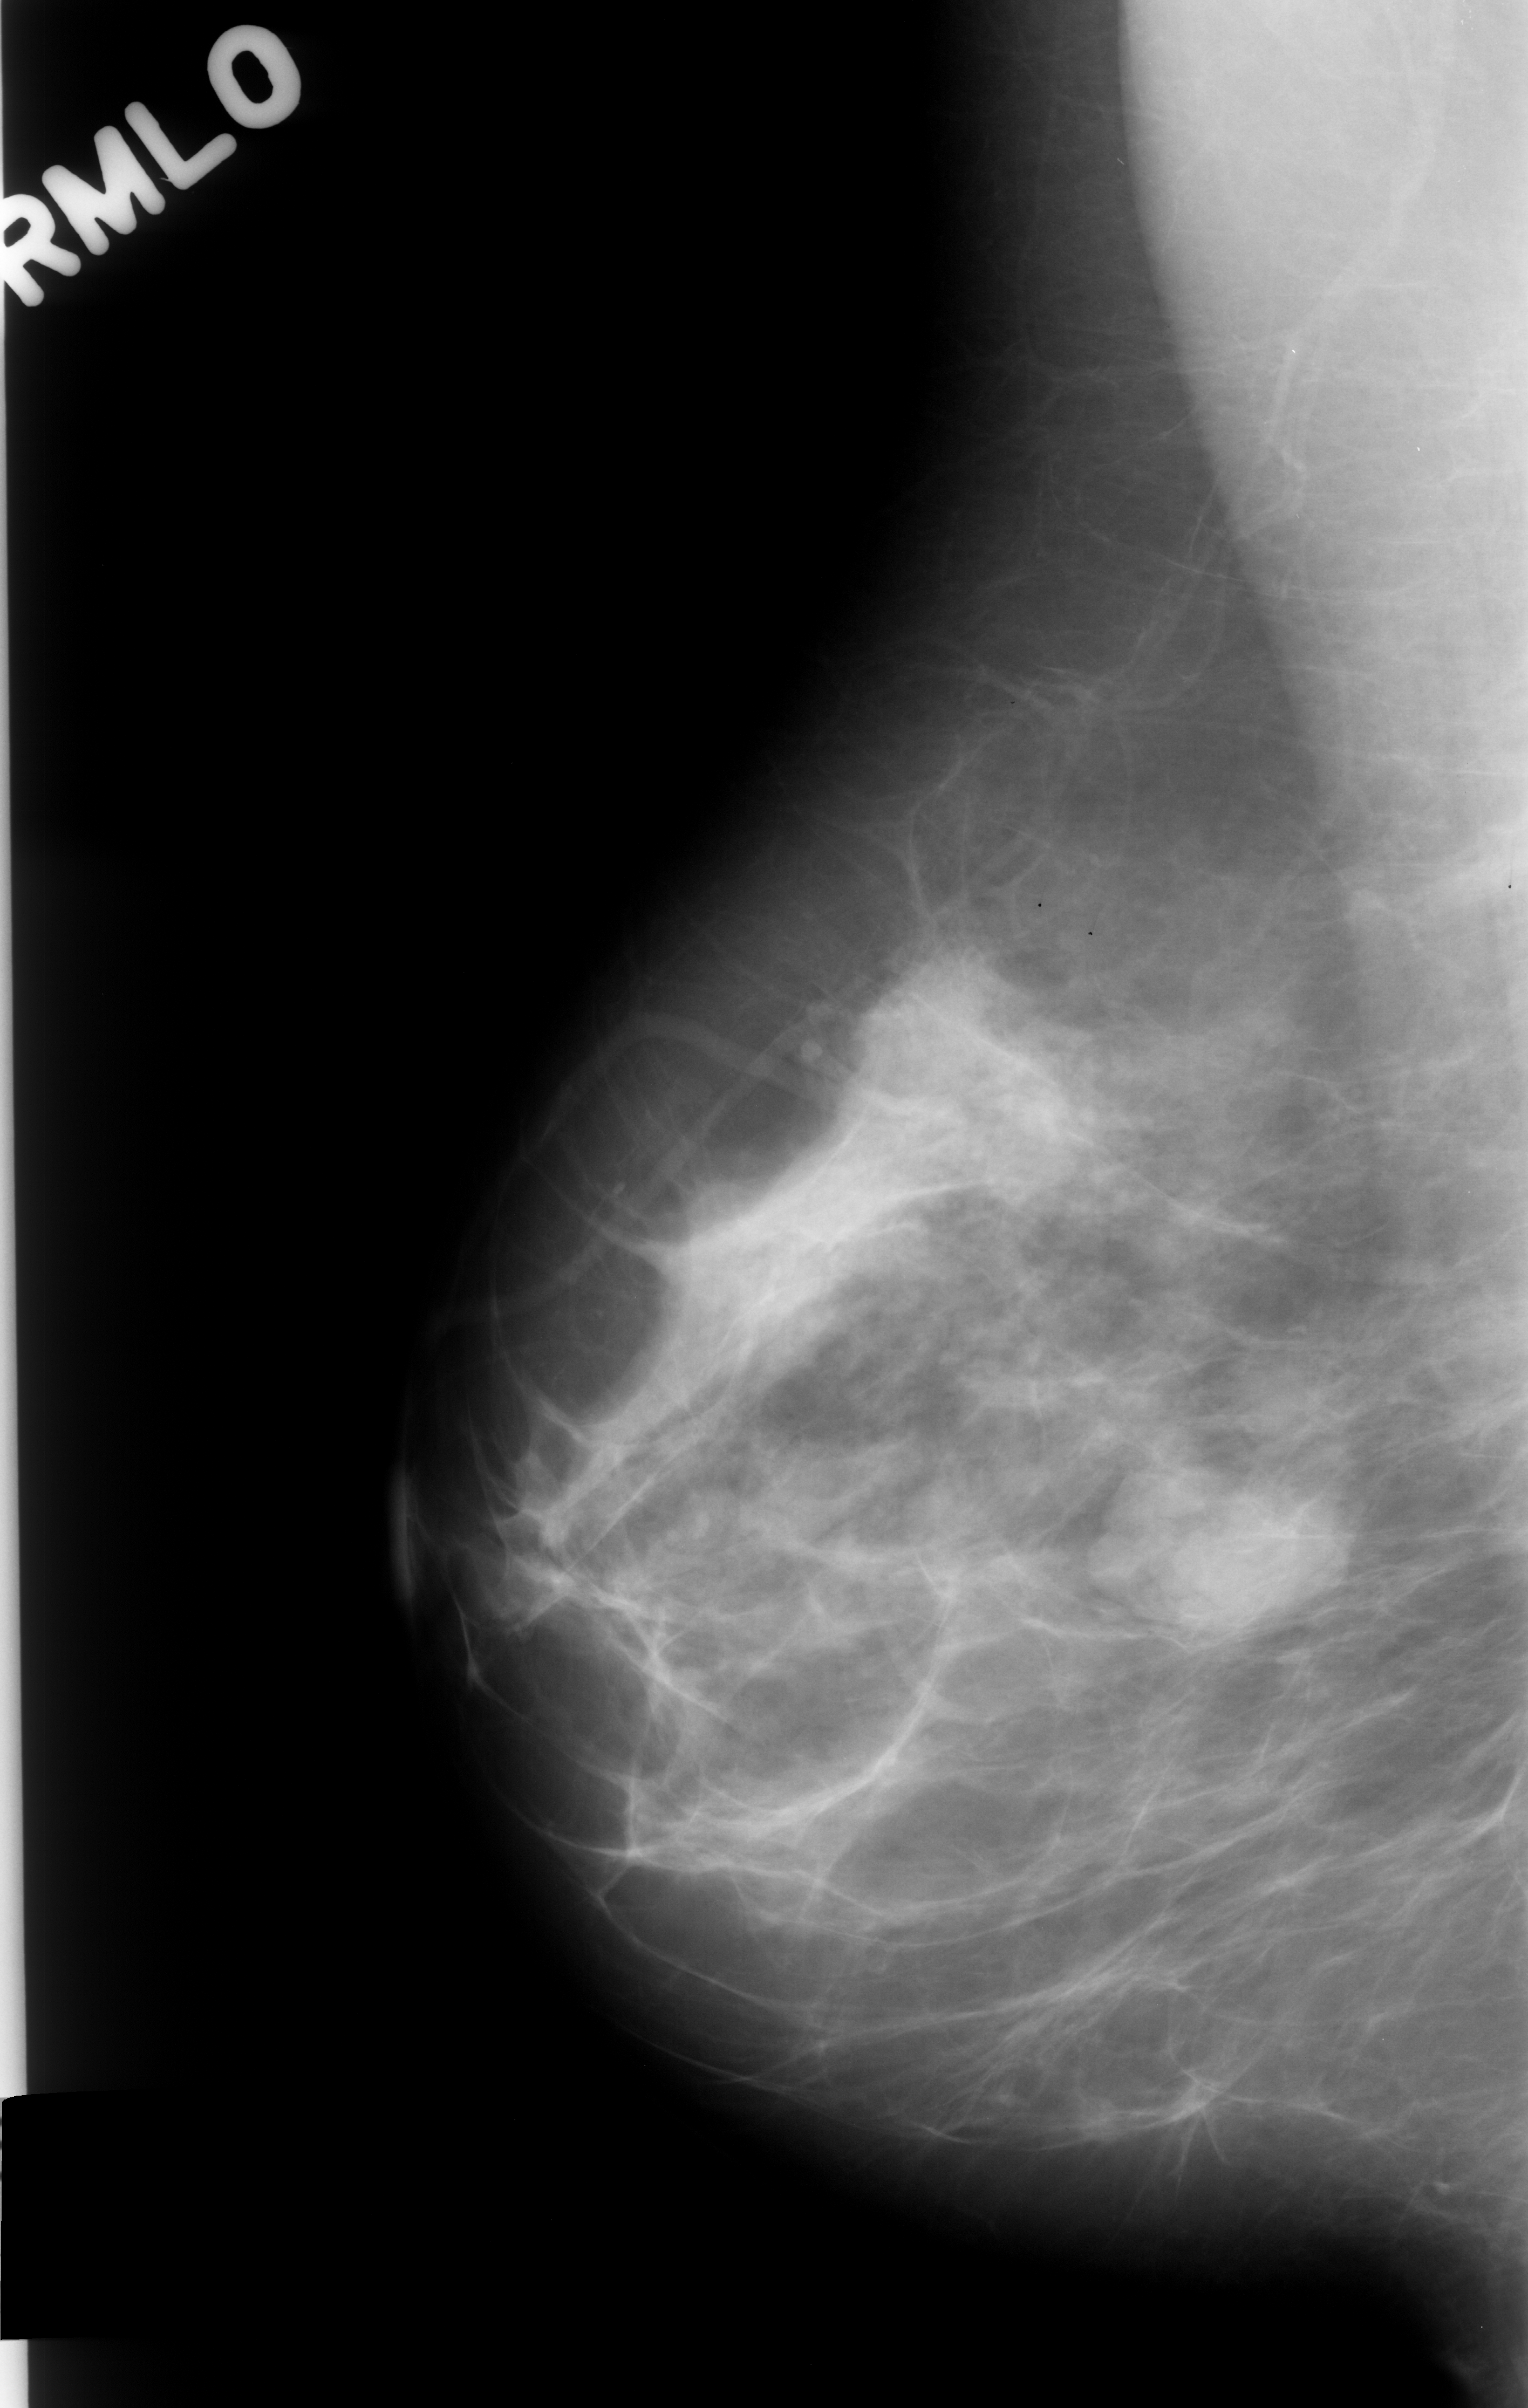
Scanned film-screen mammogram; right breast; MLO view; breast composition: scattered fibroglandular densities (BI-RADS density category 2 of 4).
- Marked findings (only marked abnormalities are described; nothing is implied about the rest of the image): mass, shape lobulated, margins circumscribed; BI-RADS assessment category 4; pathology result (as recorded, not read from the image): benign.